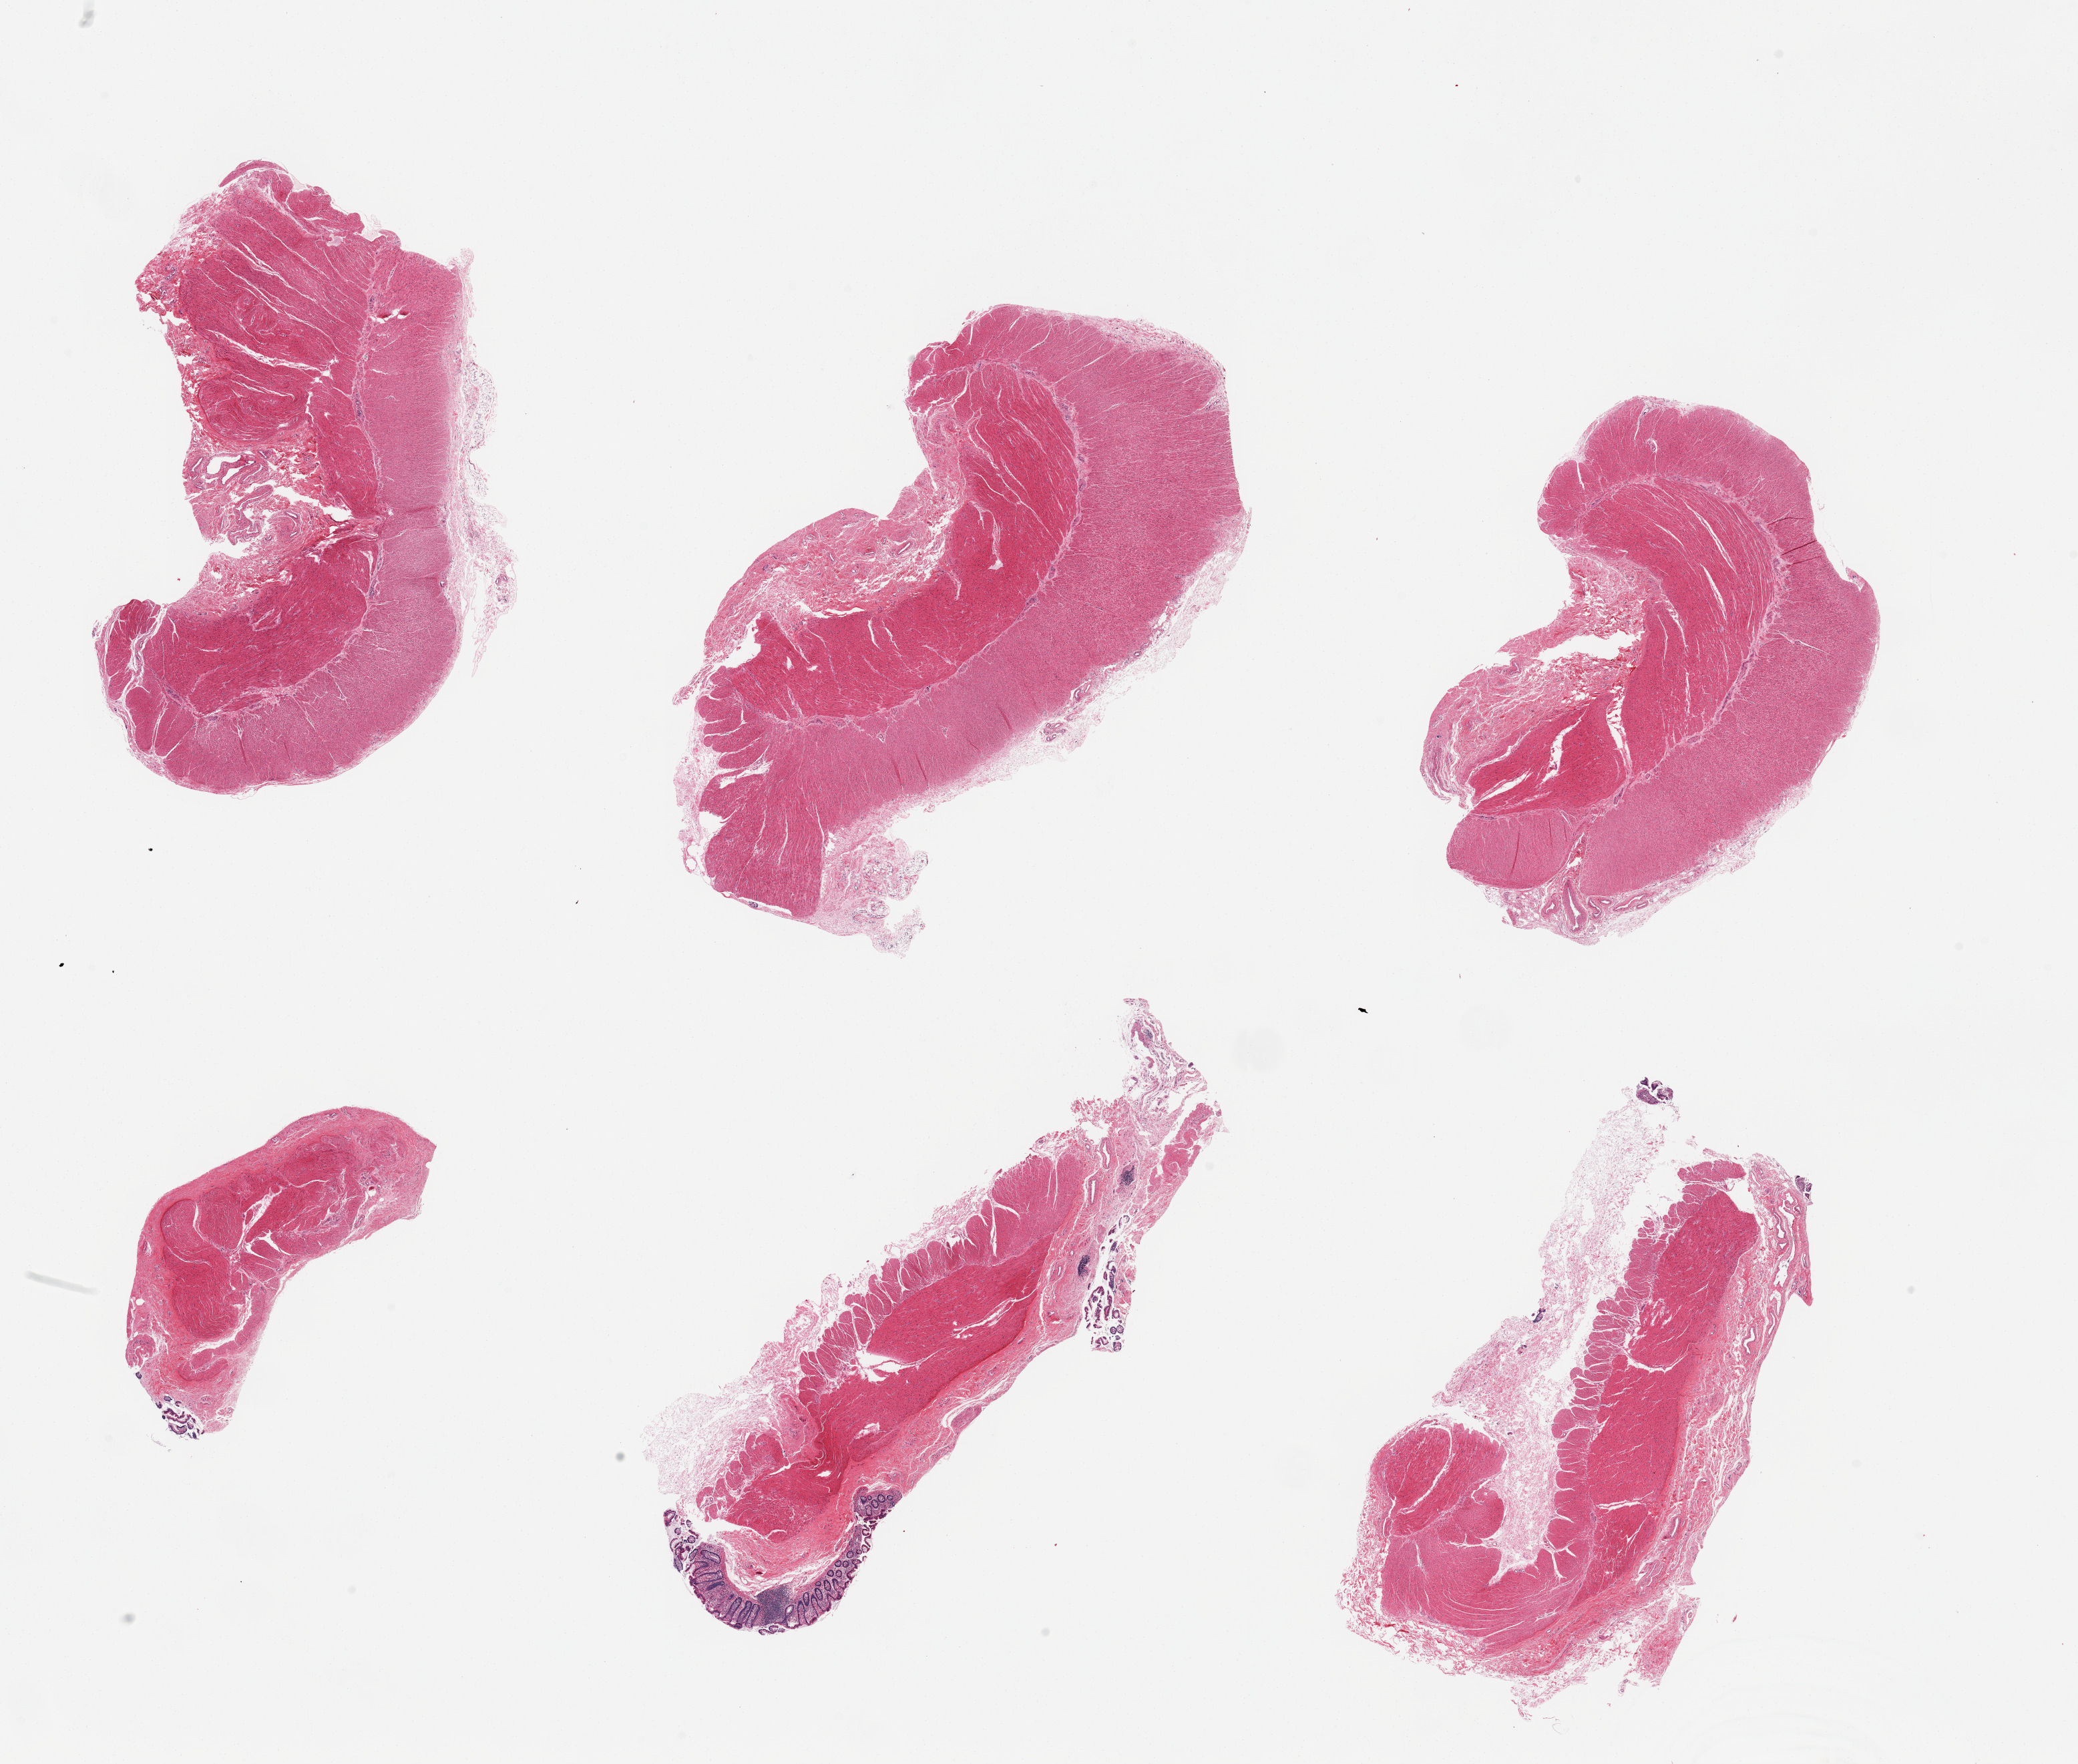
Digitized haematoxylin and eosin-stained section — shown as a low-resolution overview of the whole scanned area (about 24.6 x 20.9 mm), PAXgene-fixed, paraffin-embedded tissue, target tissue: transverse colon, tissue donor sample. Donor: female.
Pathologist's review note for this sample: 6 pieces, mucosa variably preserved but largely sloughed.